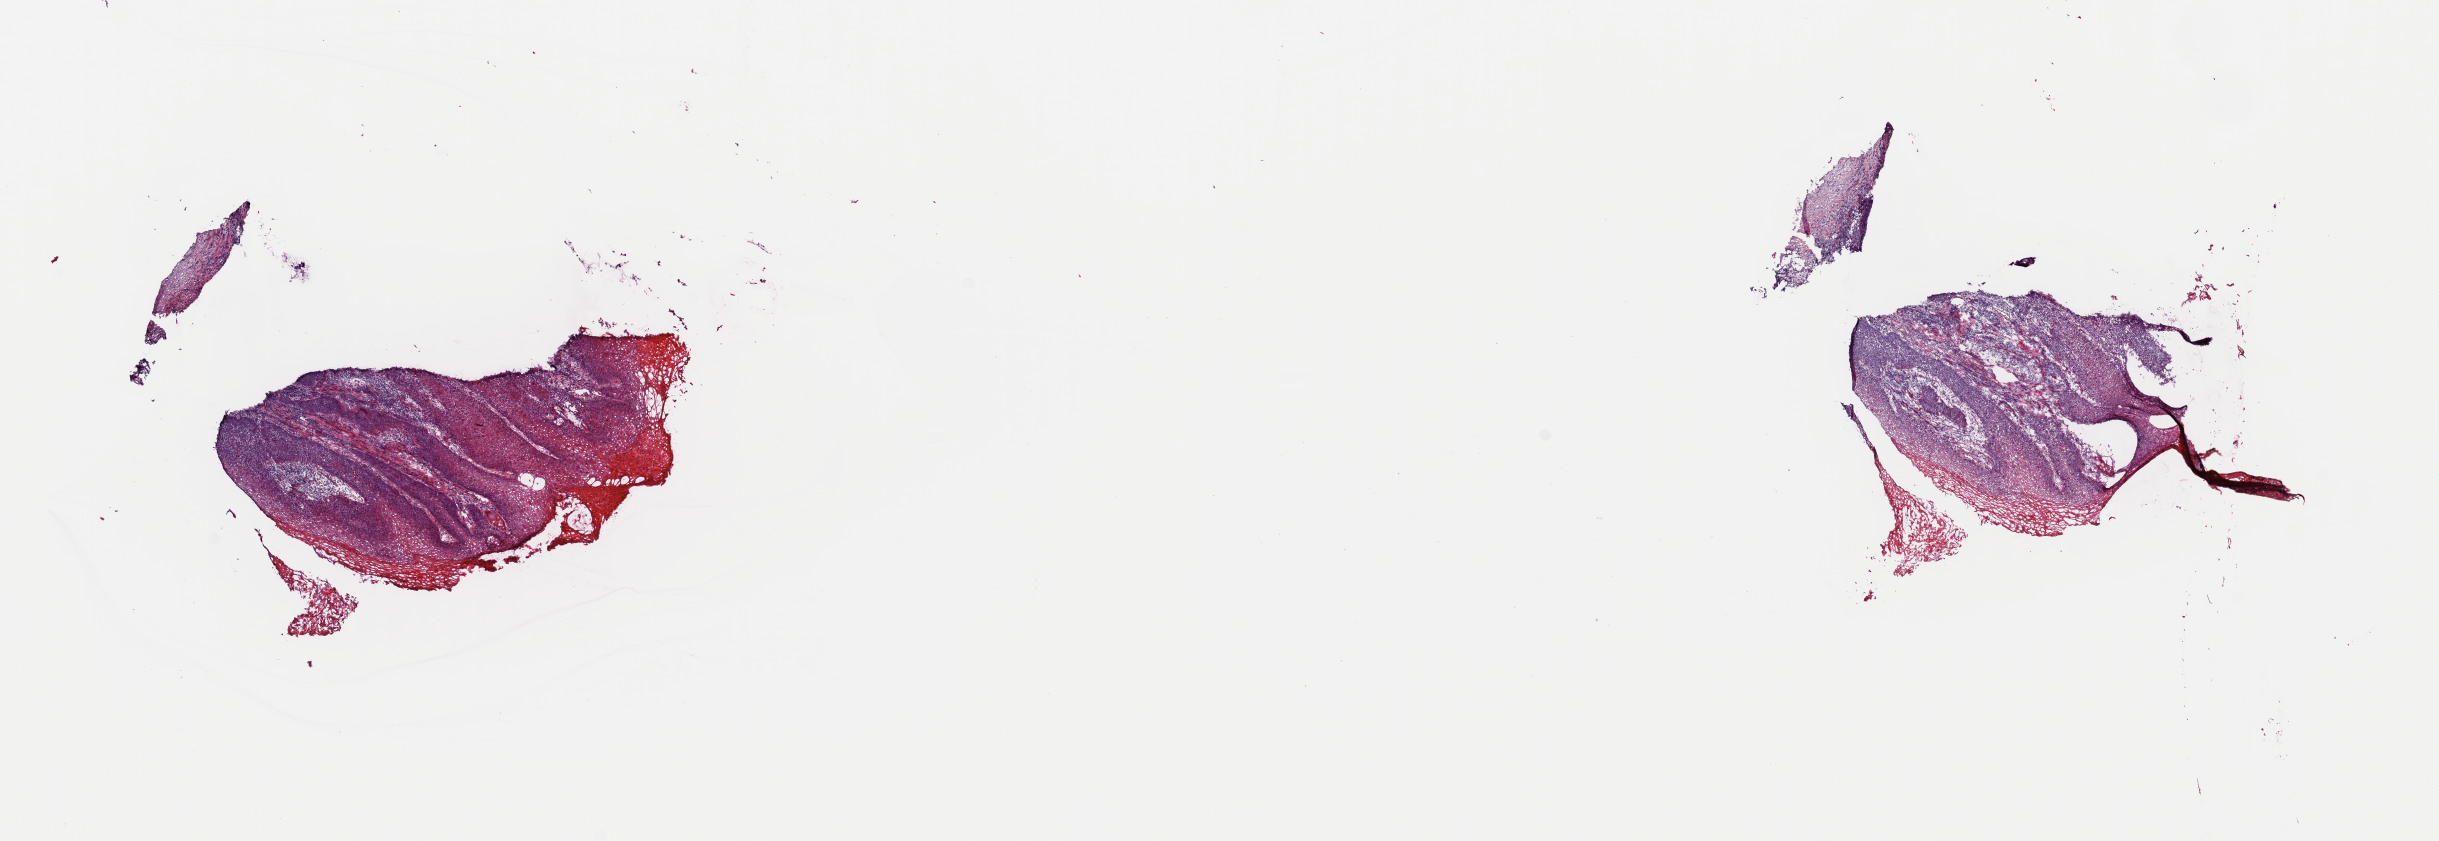
Hematoxylin and eosin (H&E) stained whole-slide image, a low-resolution overview of the entire scanned area, about 19.3 x 6.6 mm (acquisition: 40x scan), frozen section, sample: primary tumour, head and neck. Male, age 67 years at initial diagnosis. Histologic grade: G1 (well differentiated). Slide review estimates, as recorded: tumour cells 100%, tumour nuclei 75%, normal cells 0%, stromal cells 0%, necrosis 0%. Inflammatory infiltration, as recorded: lymphocyte infiltration 10%, monocyte infiltration 0%, neutrophil infiltration 0%.
AJCC pathologic stage: III (7th edition). Pathologic diagnosis: Squamous cell carcinoma, keratinizing, NOS. Lymph nodes positive (case pathology): 1 of 3 examined.